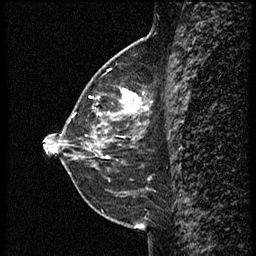
Breast MRI (dynamic contrast-enhanced), one sagittal slice. Position 24 of 60 along the scan axis. Dynamic contrast-enhanced study with each time point stored as its own series, time point 2 of 3 at this slice position (early post-contrast, ordered by acquisition time). 1.5 T. TE 4.2 ms, TR 18.9 ms. 2 mm slice thickness. 256 × 256 image matrix. Female patient. Case-level facts recorded for this patient, not image findings: setting: breast cancer imaged before/during neoadjuvant chemotherapy; receptor status: HER2-positive.
Outlined on this slice (semi-automatic segmentation, software-assisted and operator-edited):
- analysis volume of interest (the breast-tissue region the enhancement analysis was run in; not a lesion): bounding box [x1, y1, x2, y2] px = [77, 87, 156, 147]
- tumour enhancement mask (voxels above the 100 % enhancement threshold inside the analysis volume of interest): [87, 89, 151, 147]